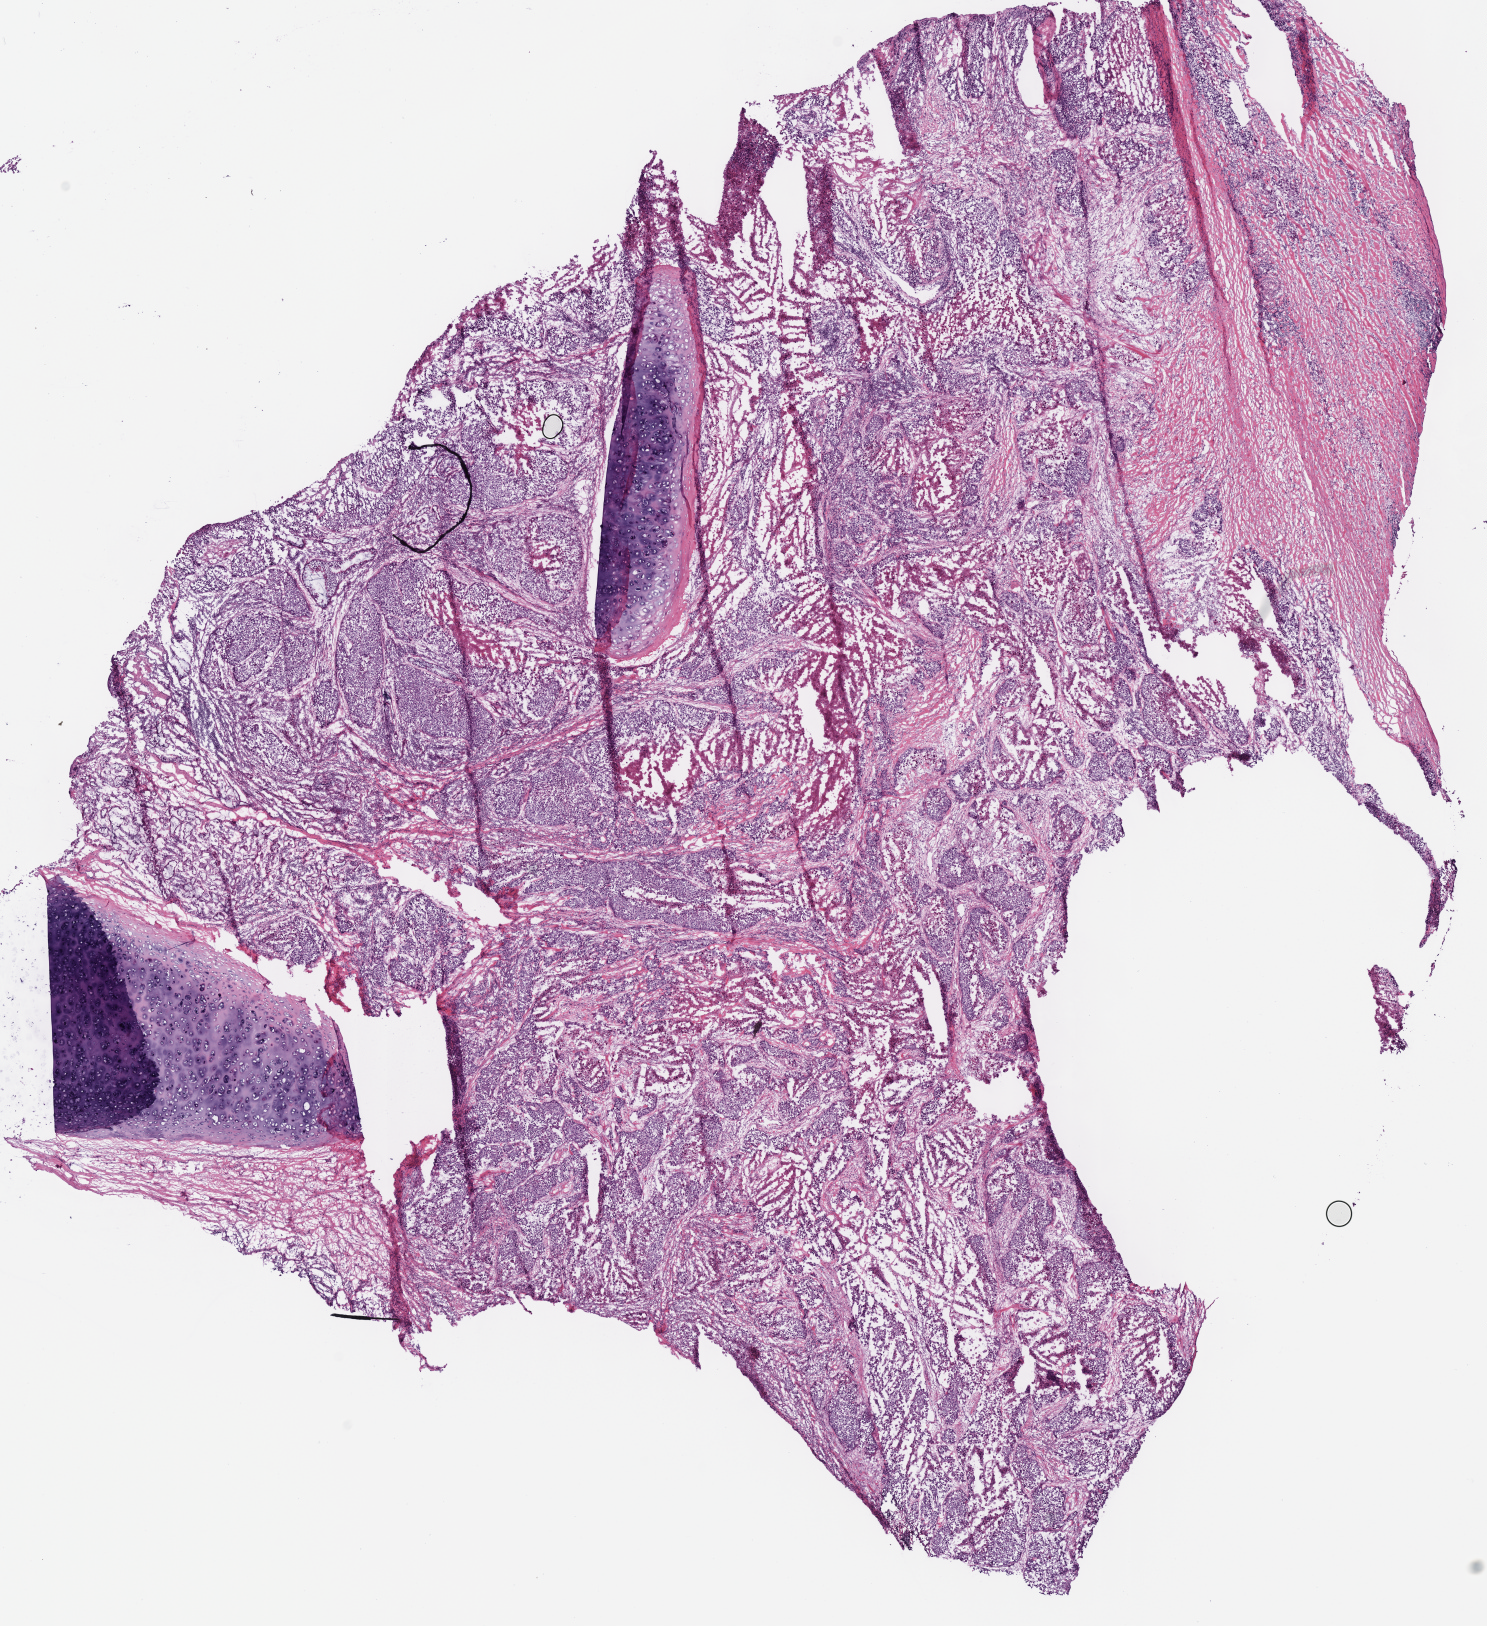
Whole-slide histology image, H&E — whole scanned area (about 11.7 x 12.8 mm, from a 40x scan) shown as a low-resolution overview; frozen section from the bottom of the tissue portion; primary tumour sample from the lung. Patient: male, age at initial diagnosis 50 years. Pathologist review of this section (percent, as recorded): tumour cells 85%, tumour nuclei 70%, normal cells 15%, stromal cells 0%, necrosis 0%. Infiltration values recorded for this section: lymphocyte infiltration 15%, monocyte infiltration 0%, neutrophil infiltration 0%.
* histologic diagnosis: Squamous cell carcinoma, NOS (upper lobe, lung)
* AJCC pathologic stage: IIA (7th edition)
* laterality: left